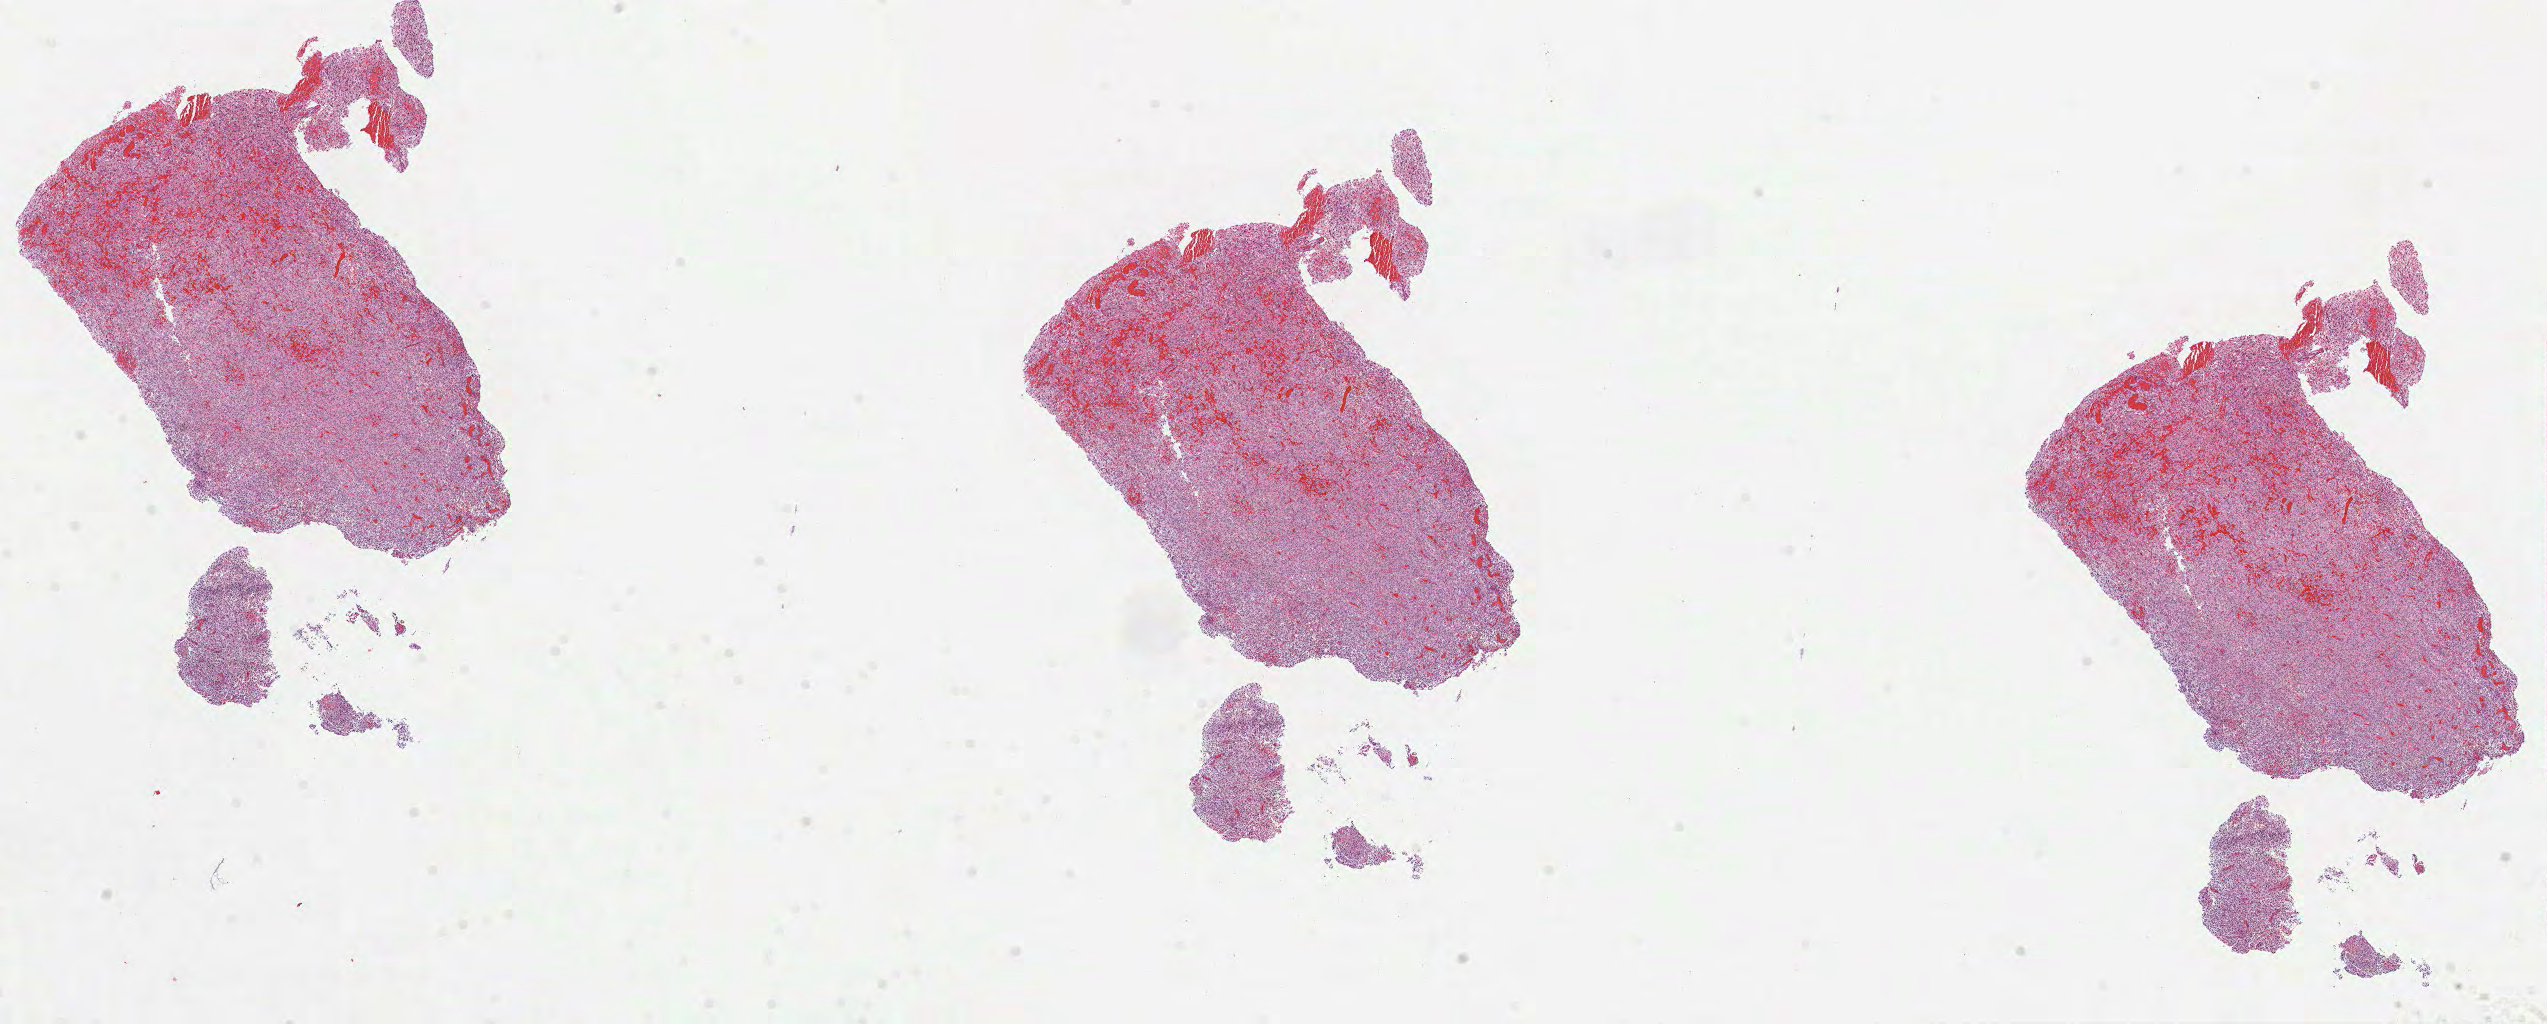
Digitized Hematoxylin and eosin (H&E) stained tissue section (whole slide) — a low-resolution overview of the entire scanned area, about 20.5 x 8.3 mm (from a 40x scan). Formalin-fixed paraffin-embedded (FFPE) diagnostic section. Brain, primary tumour sample. Female patient; age at initial diagnosis 78 years.
Pathologic diagnosis: Glioblastoma.